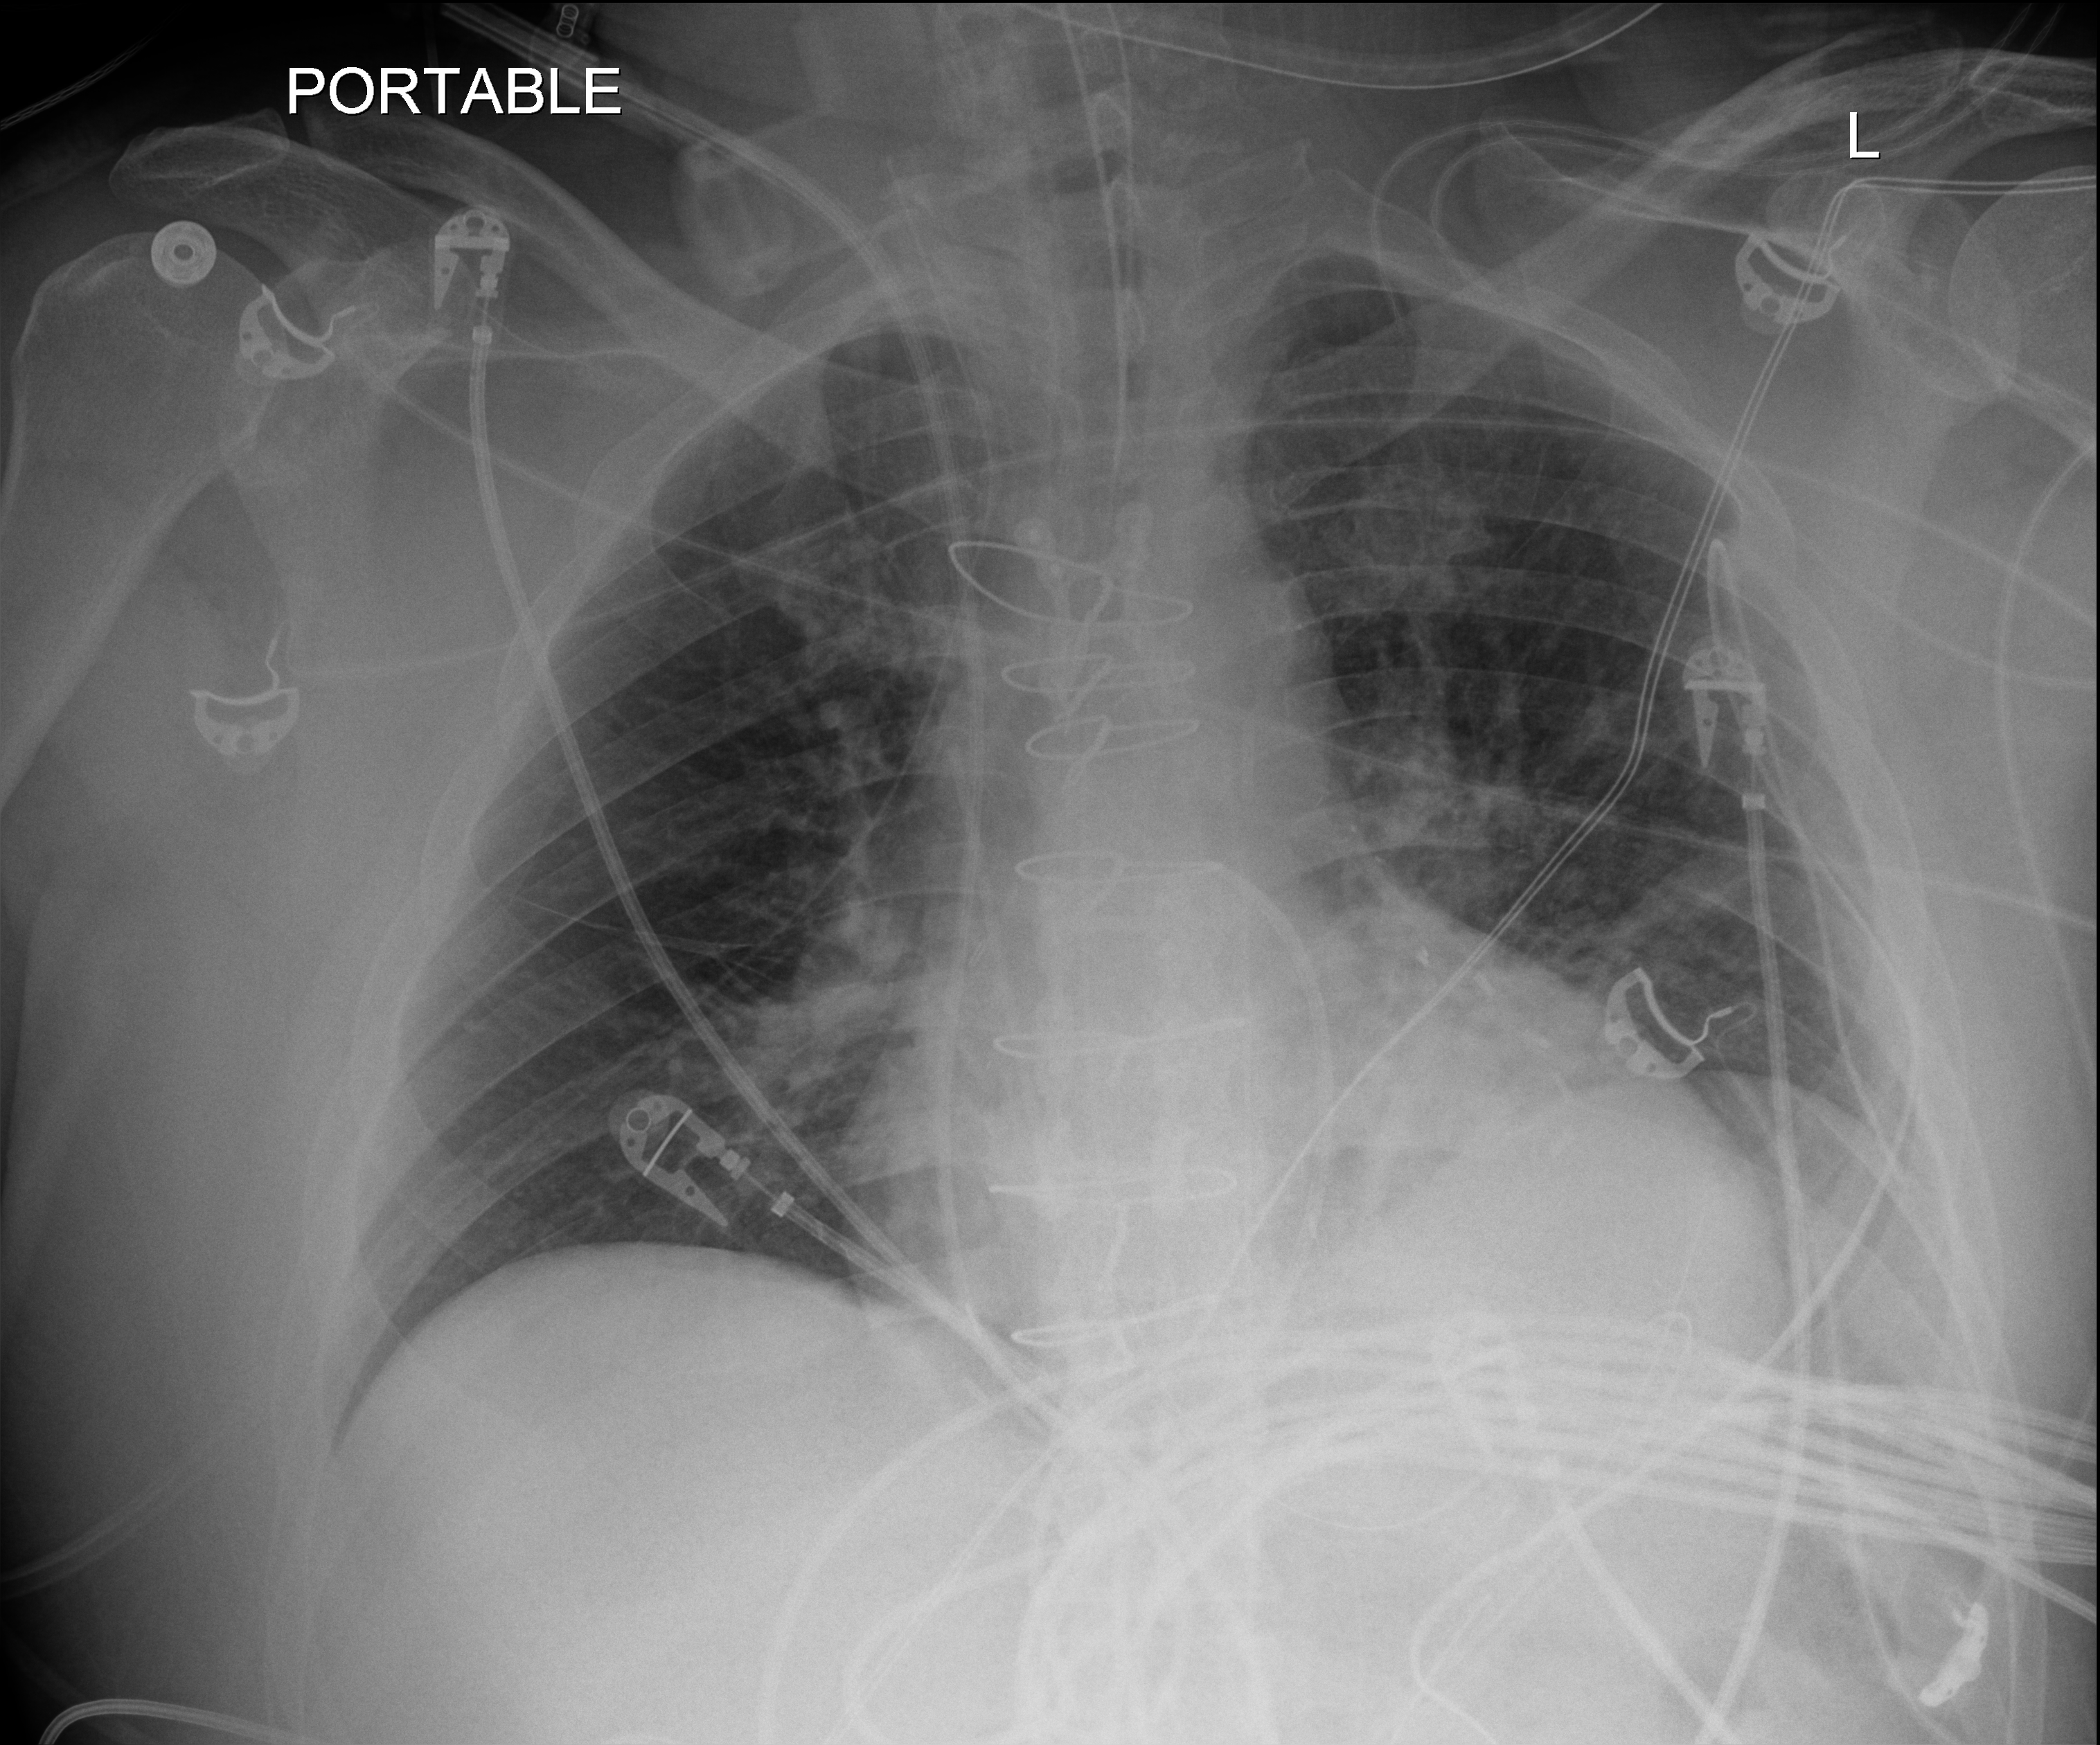
Portable chest radiograph; anteroposterior (AP) projection. Patient hospitalised with COVID-19; male, aged 18–59 years.
From the hospital-stay record, not from the radiograph (when in the stay this image was taken is not recorded): admitted to intensive care during this hospital stay: no; mechanically ventilated during this hospital stay: no.